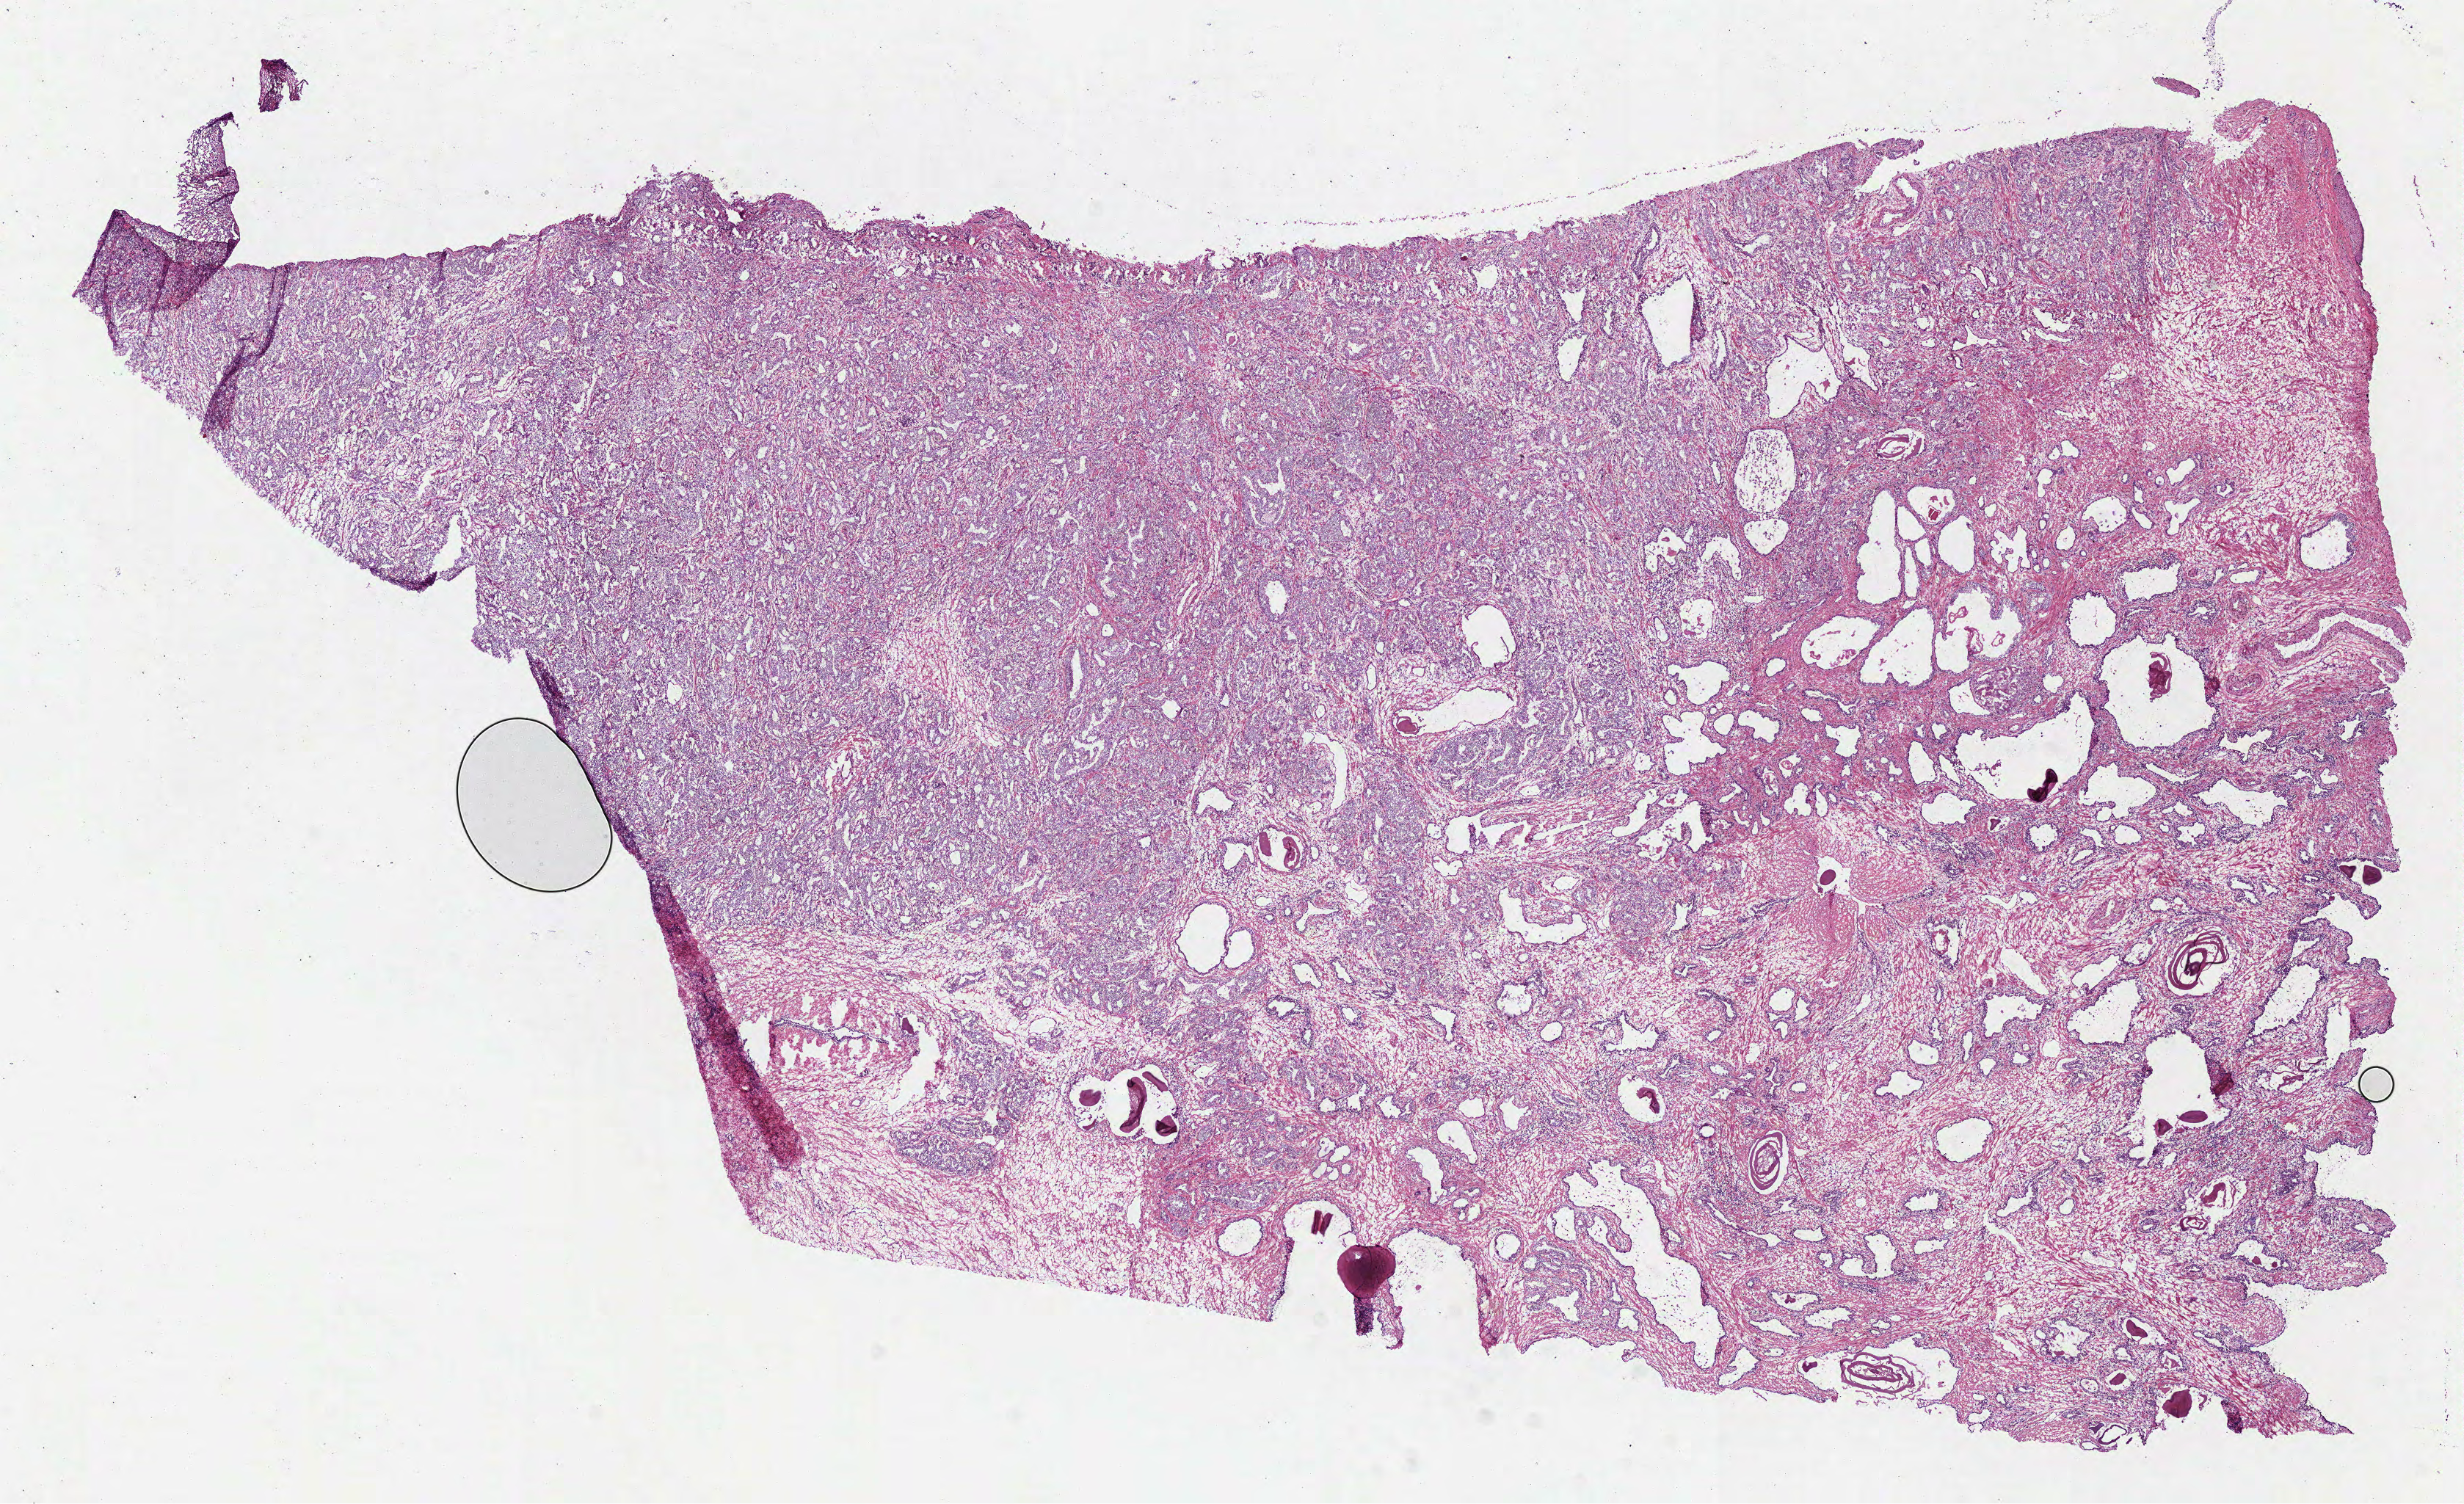
Whole-slide histology image, H&E — whole scanned area (about 13.5 x 8.3 mm, from a 40x scan) shown as a low-resolution overview. Frozen section. Sample: primary tumour, prostate. Male patient; age at initial diagnosis 63 years. Gleason score: 8 (4+4). Pathologist review of this section (percent, as recorded): tumour cells 65%, tumour nuclei 65%, normal cells 25%, stromal cells 10%, necrosis 0%.
Lymph nodes positive (case pathology): 0 of 7 examined. Laterality: left. Histologic diagnosis: Acinar cell carcinoma (prostate gland).